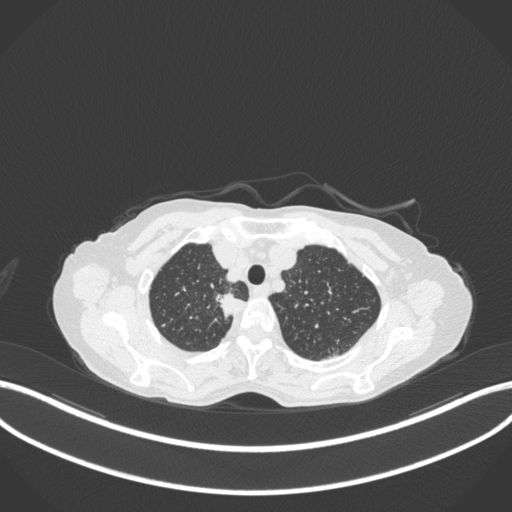
Chest CT, one axial slice; position 315 of 363 along the scan axis; 120 kVp; lung window (W 1500 / L -600 HU); 1 mm slice thickness; 512 × 512 image matrix, field of view 400 × 400 mm. Female patient, age 75 years. From the clinical record (not read from this slice): clinical TNM (as recorded): T1c N1 M1.
Annotated regions visible in this slice (bounding box drawn by a radiologist):
- lung tumour (recorded histology: adenocarcinoma): bounding box (x1, y1, x2, y2) in pixels: (210, 288, 255, 324)